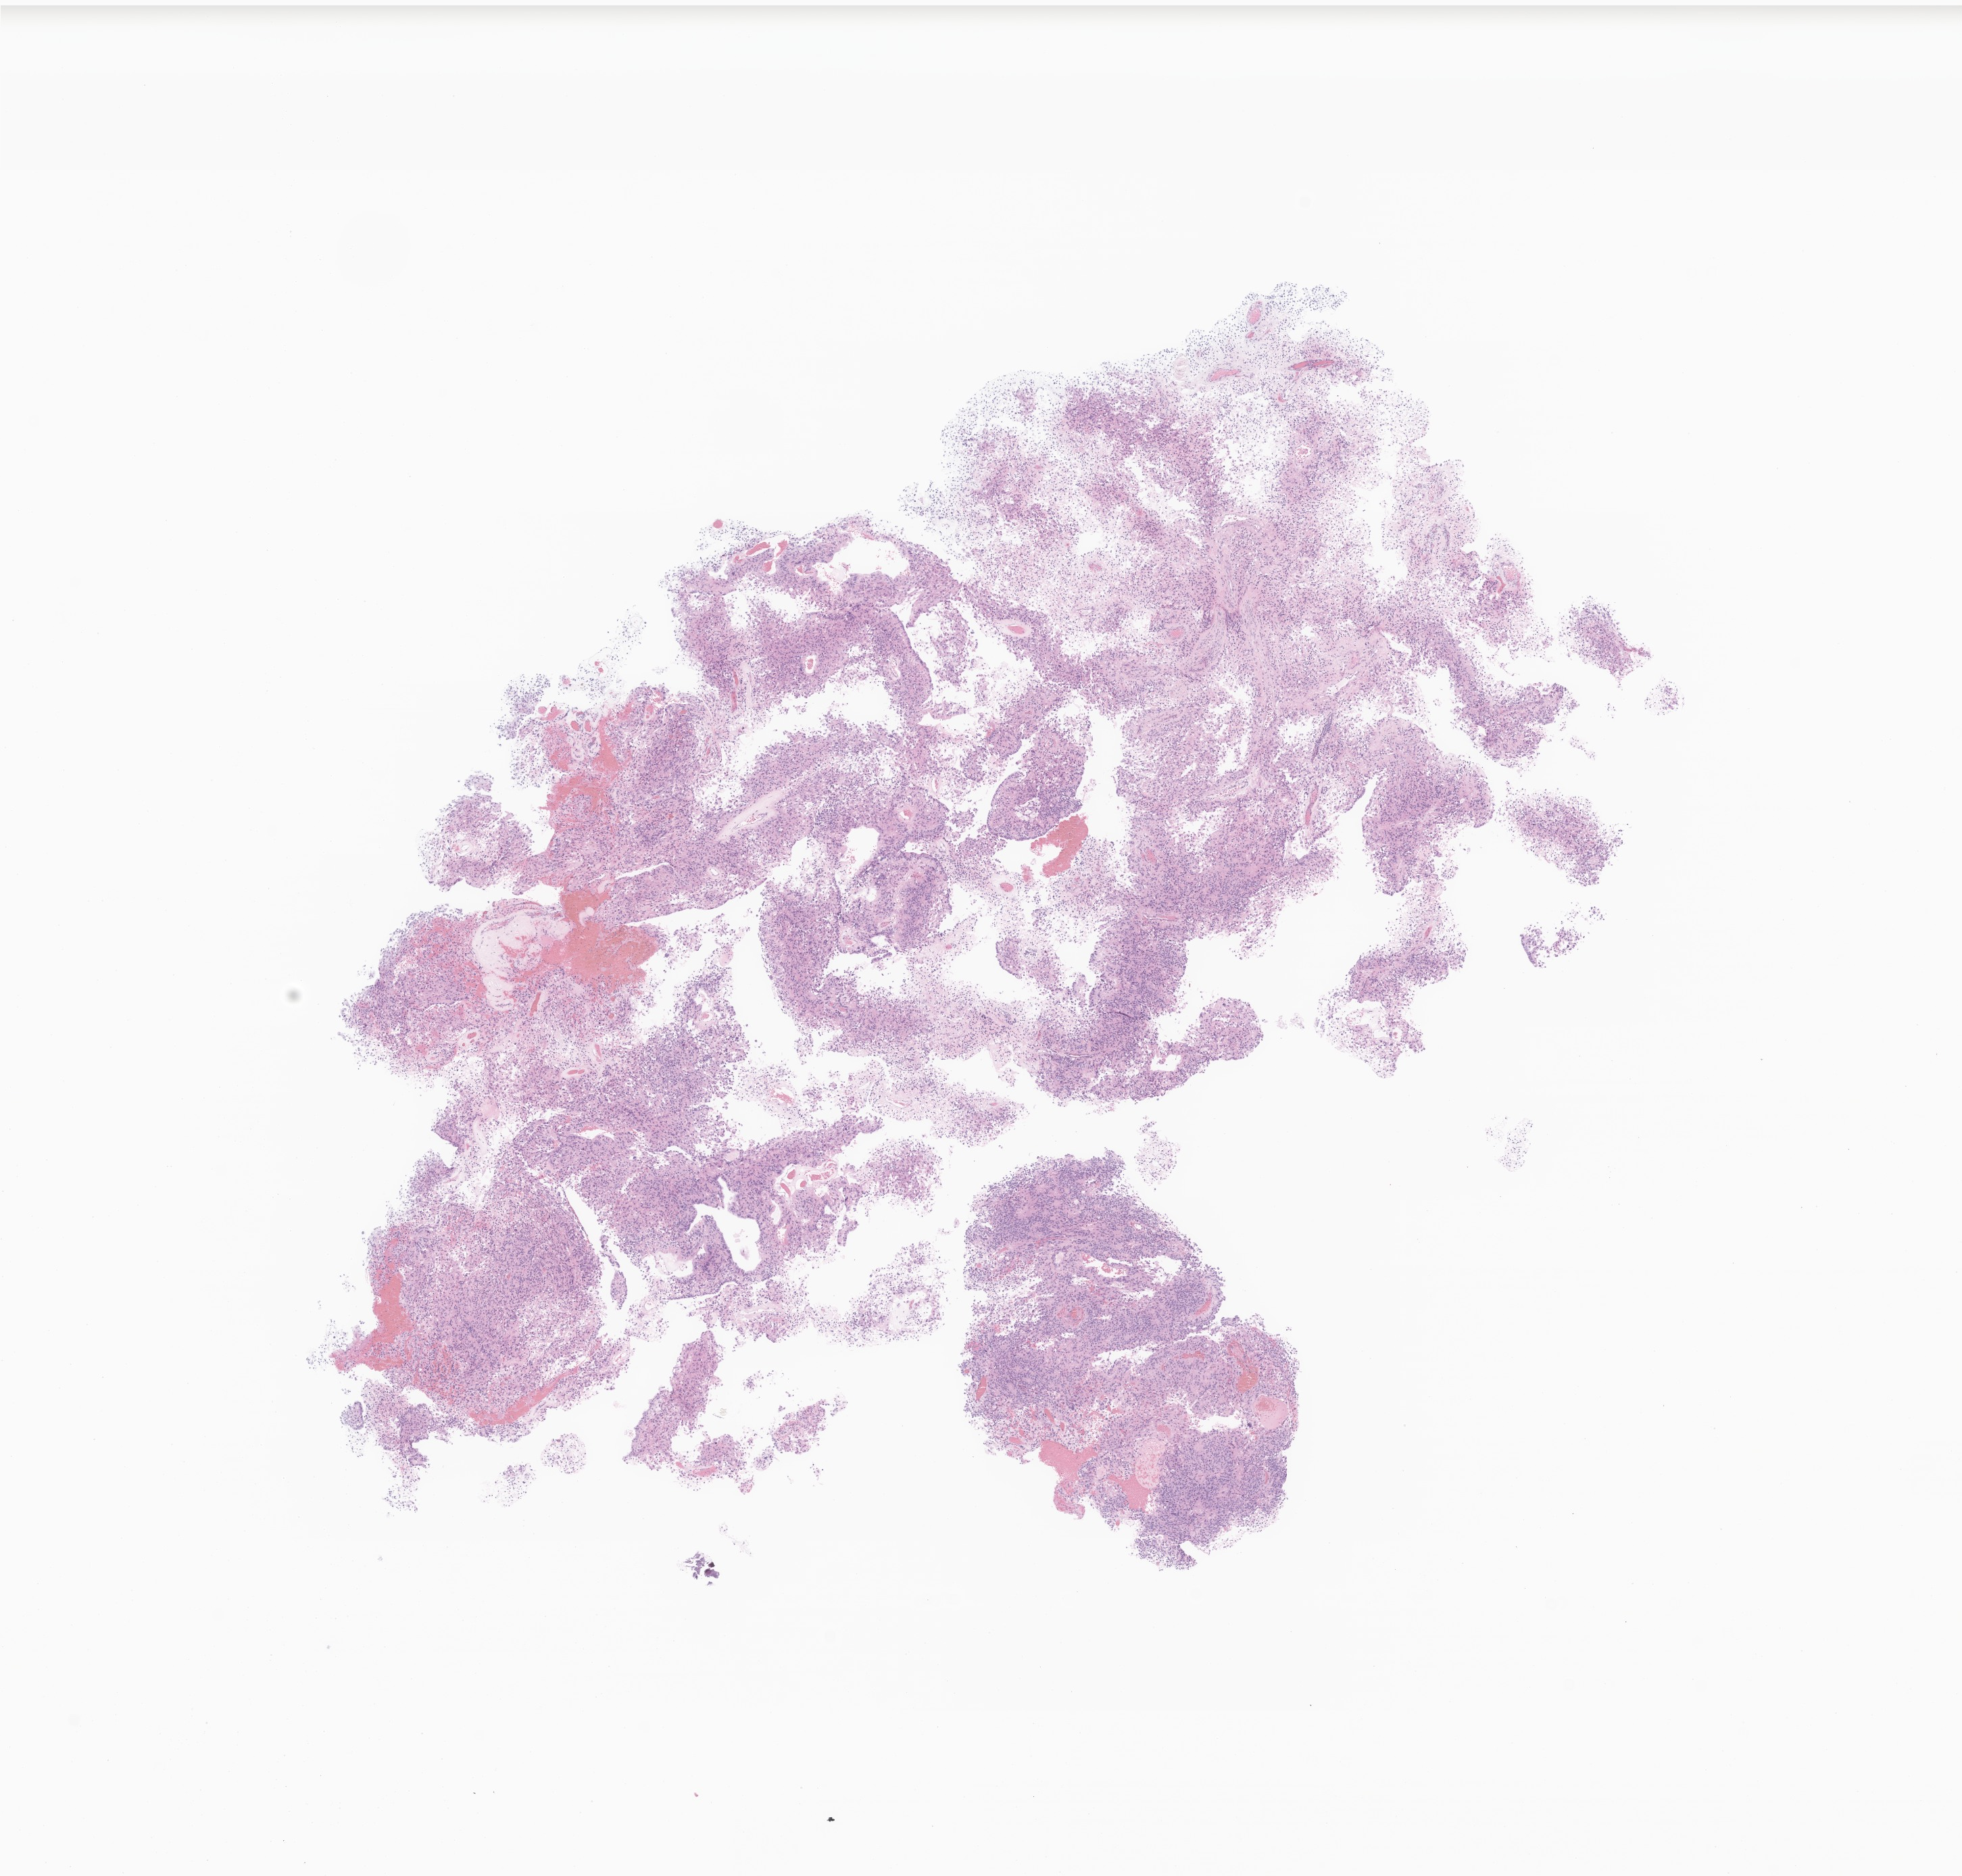
Digitized hematoxylin and eosin (H&E)-stained section of tumor tissue from the brain, a low-resolution overview of the entire scanned area, about 12.2 x 11.7 mm. Formalin-fixed paraffin-embedded section. Patient: male, age 149 months (12 years 5 months).
• diagnosis: Ependymoma, NOS